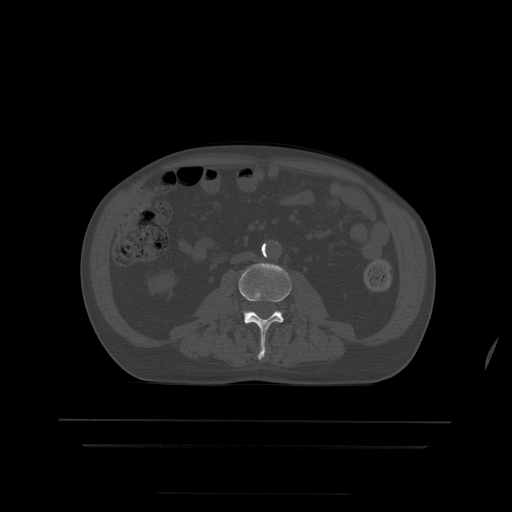
CT including the spine, one axial slice. Slice 117 of 522 in the series (ordered by position). Bone window (W 1800 / L 400 HU). 1.25 mm slice thickness. 512 × 512 image matrix, field of view 436 × 436 mm. Patient age 68 years. From the clinical record (not read from this slice): primary cancer: urothelial.
Annotated regions visible in this slice (semi-automatic segmentation, software-assisted and operator-edited):
- L3 vertebra: bounding box (x1, y1, x2, y2) in pixels: (239, 264, 292, 360)